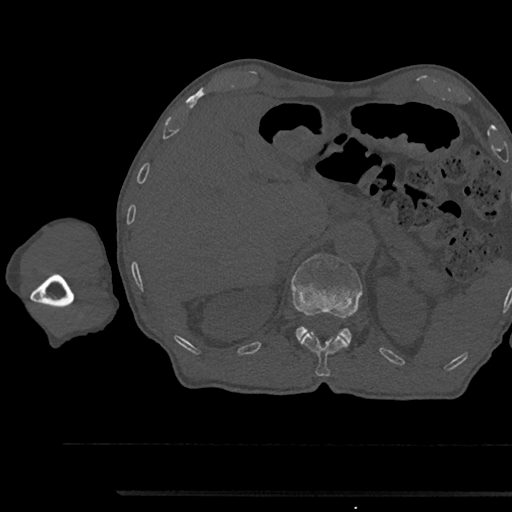
CT including the spine, one axial slice; slice 680 of 797 in the series (ordered by position); 120 kVp; bone window (W 1800 / L 400 HU); 0.5 mm slice thickness; 512 × 512 image matrix, field of view 367 × 367 mm. Male patient, age 79 years. From the clinical record (not read from this slice): primary cancer: prostate.
Annotated regions visible in this slice (semi-automatic segmentation, software-assisted and operator-edited):
- L1 vertebra: bounding box (x1, y1, x2, y2) in pixels: (291, 254, 362, 342)
- T12 vertebra: (300, 332, 349, 377)